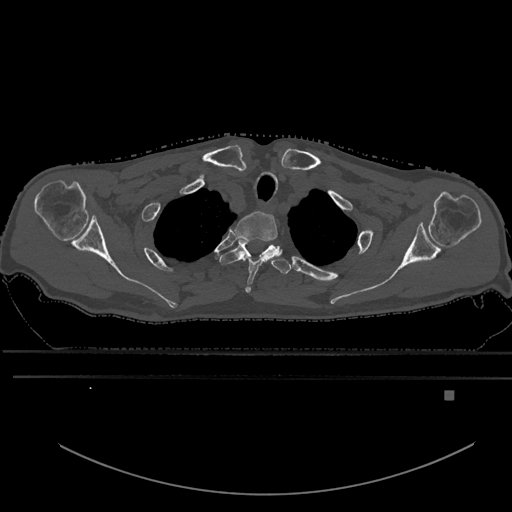
CT including the spine, one axial slice. Slice 513 of 969 in the series (ordered by position). Bone window (W 1800 / L 400 HU). 0.5 mm slice thickness. 512 × 512 image matrix. Patient: male, 82 years. Case-level facts recorded for this patient, not image findings: primary cancer: prostate.
Structures marked on this image (semi-automatic segmentation, software-assisted and operator-edited):
- T1 vertebra: bounding box <234,211,279,293> (left, top, right, bottom; pixels)
- T2 vertebra: <220,239,289,274>